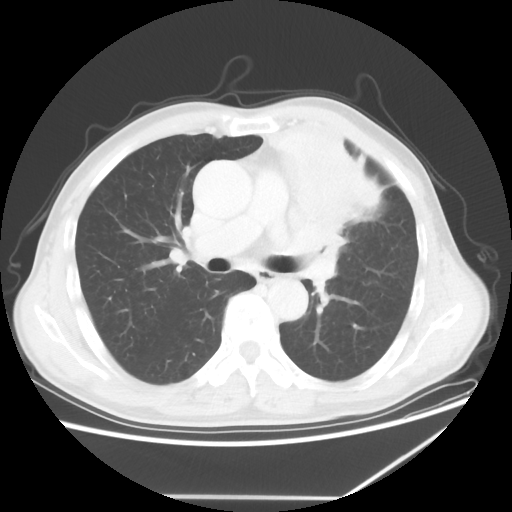
Chest CT, one axial slice. Slice 37 of 64 in the series (ordered by position). Reconstruction kernel STANDARD. 100 kVp. Lung window (W 1500 / L -600 HU). 5 mm slice thickness. 512 × 512 image matrix. Male patient, age 64 years. From the clinical record (not read from this slice): clinical TNM (as recorded): T1c N1 M1.
Outlined on this slice (bounding box drawn by a radiologist):
- lung tumour (recorded histology: squamous cell carcinoma): bounding box <282,122,399,250> (left, top, right, bottom; pixels)